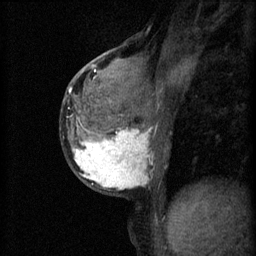
Breast MRI (dynamic contrast-enhanced), one sagittal slice; 3 images stored at this slice position (order not interpretable as contrast timing); 1.5 T; TE 4.2 ms, TR 11 ms; 2 mm slice thickness; 256 × 256 image matrix. Patient: female, 37 years.
Annotated regions visible in this slice (semi-automatic segmentation, software-assisted and operator-edited):
- analysis volume of interest (the breast-tissue region the enhancement analysis was run in; not a lesion): bounding box [x1, y1, x2, y2] px = [68, 118, 160, 195]
- tumour enhancement mask (voxels above the 70 % enhancement threshold inside the analysis volume of interest): [73, 118, 153, 189]